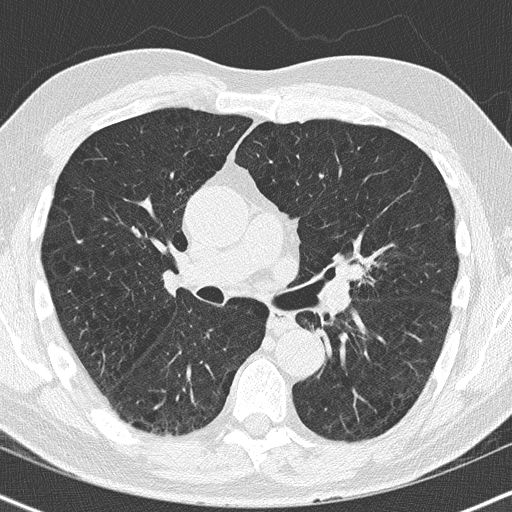
Low-dose screening chest CT, one axial slice. Position 91 of 163 along the scan axis. Reconstruction kernel B50f. Lung window (W 1500 / L -600 HU). 2 mm slice thickness. 512 × 512 image matrix, field of view 320 × 320 mm.
Structures marked on this image (expert manual segmentation):
- lesion 1 (tumor, upper lobe of left lung): box from (x=335, y=261) to (x=367, y=283) px